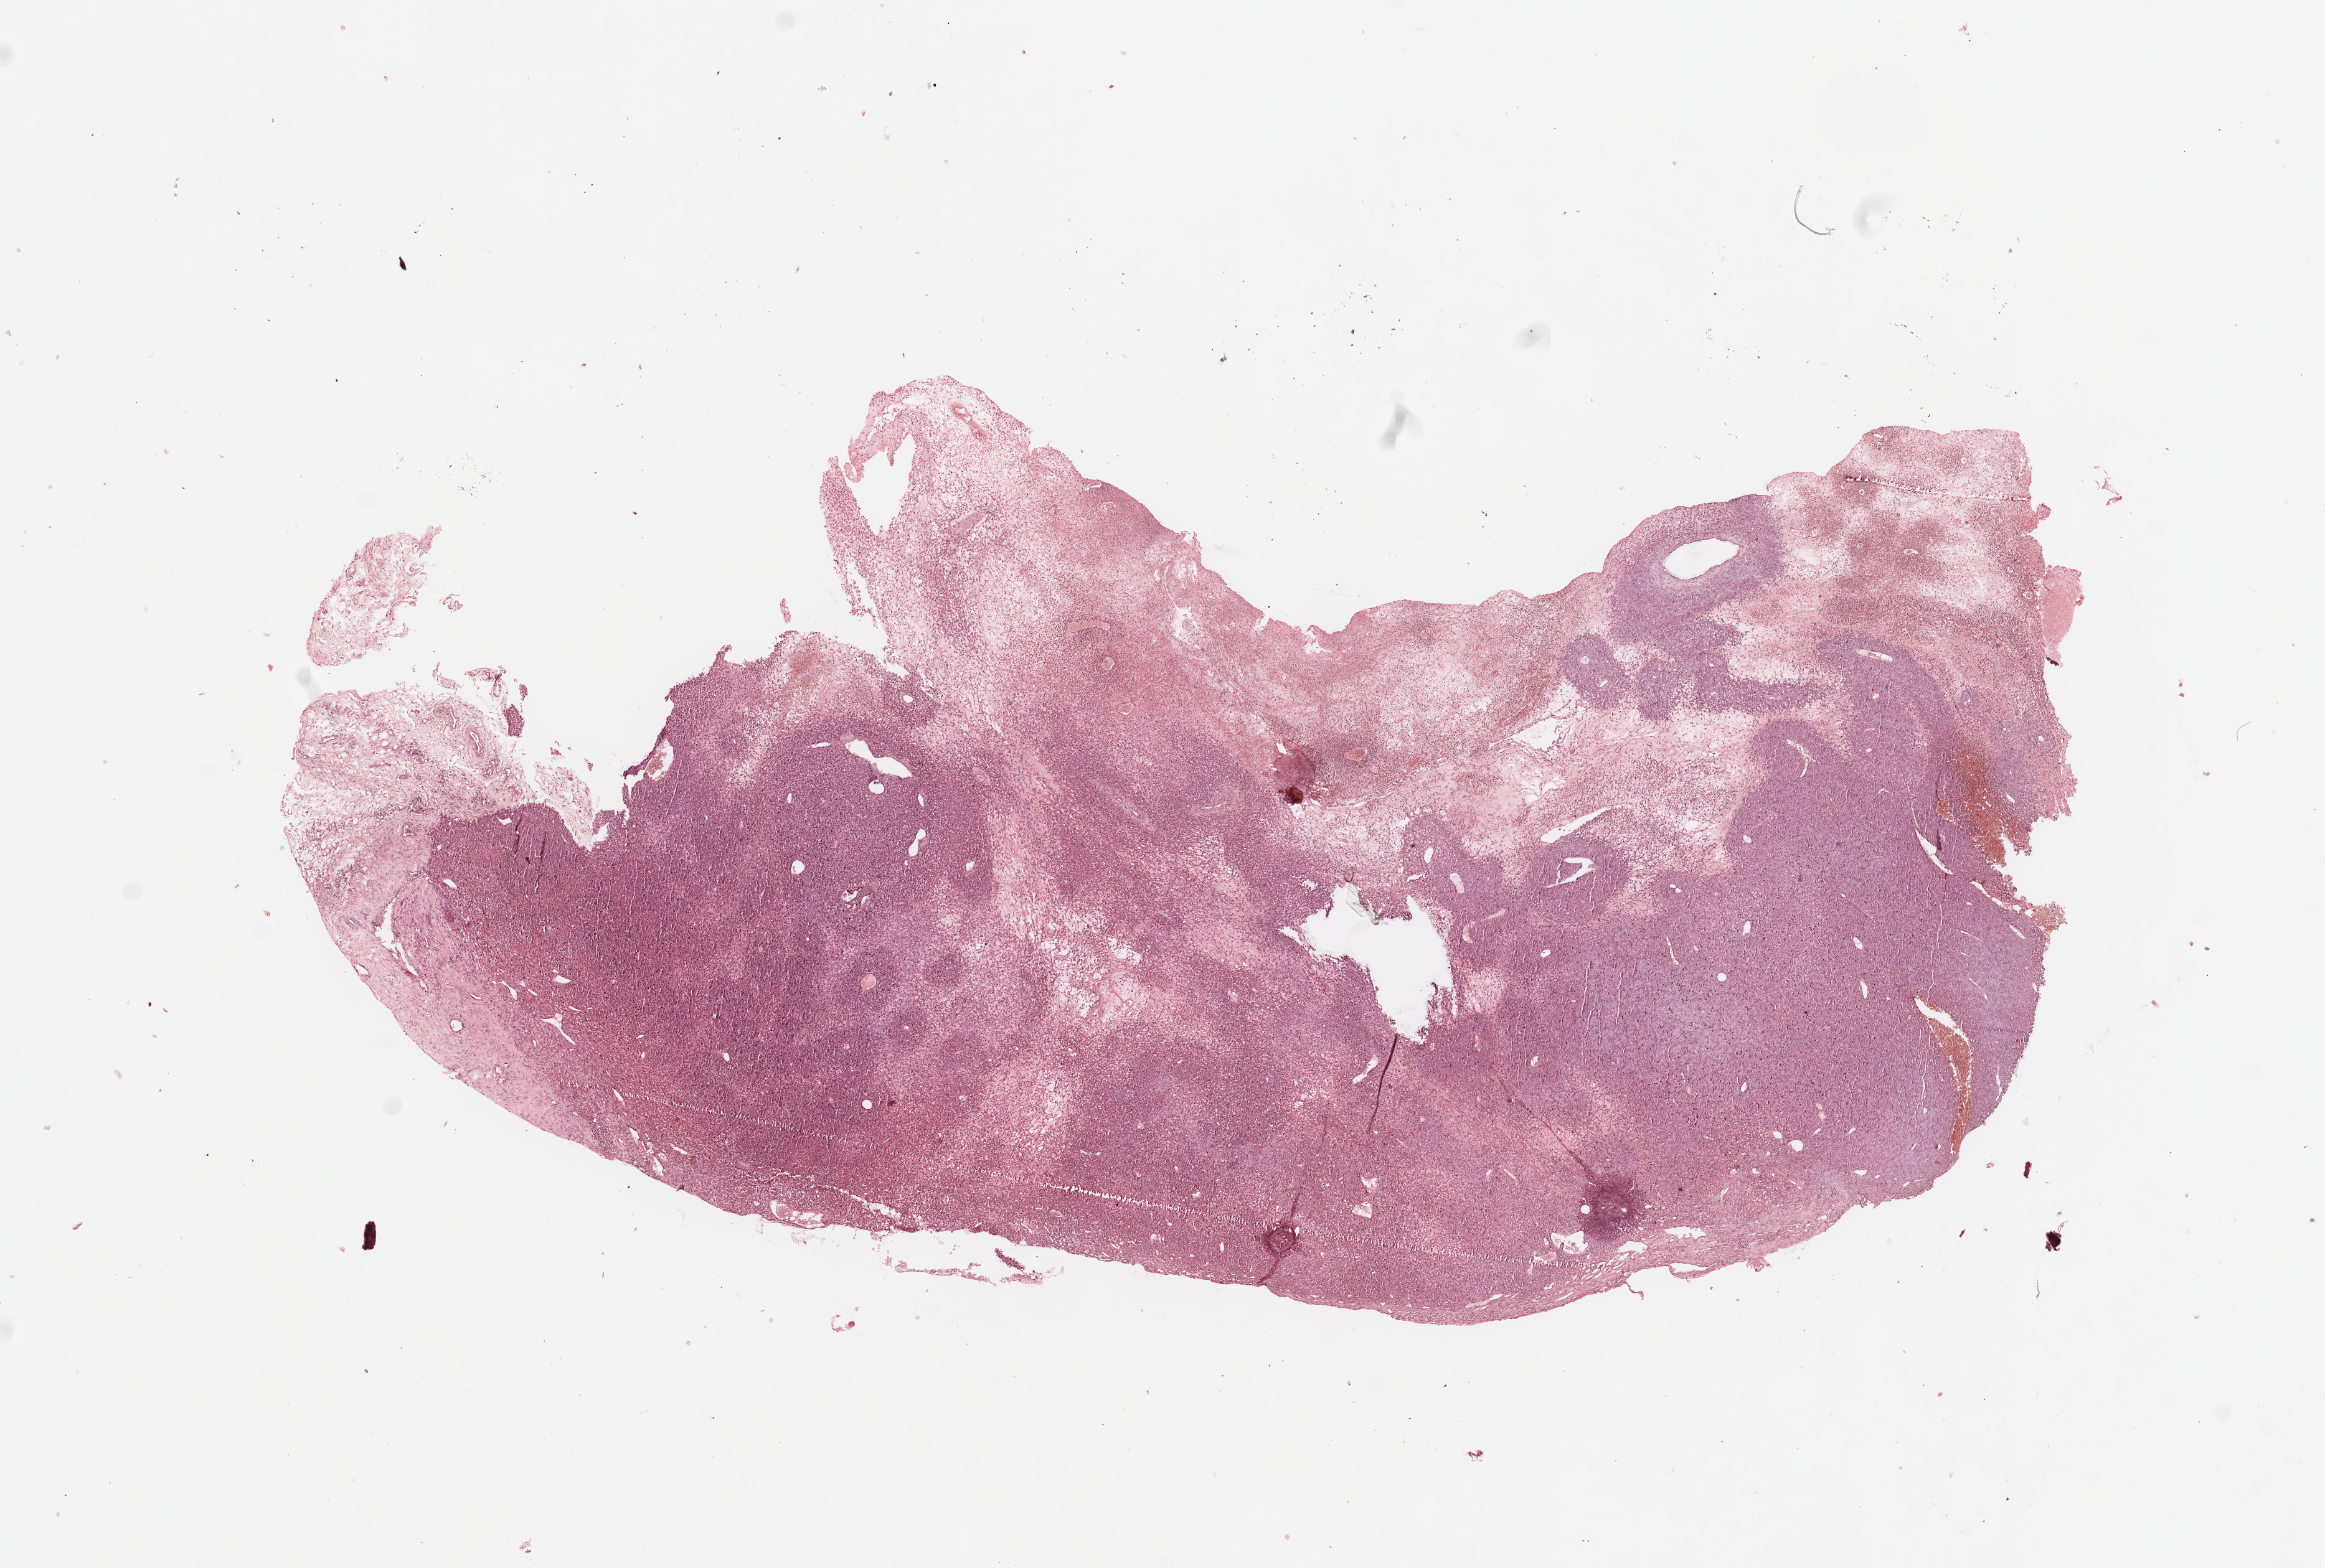
Whole-slide histology image, H&E-stained — whole scanned area (about 14.8 x 10.0 mm) shown as a low-resolution overview. Melanoma tumour tissue; sampled site not recorded. Female, 76 y/o.
Primary tumour site (as recorded): trunk. Diagnosis: Malignant melanoma, NOS. AJCC pathologic stage: IB.